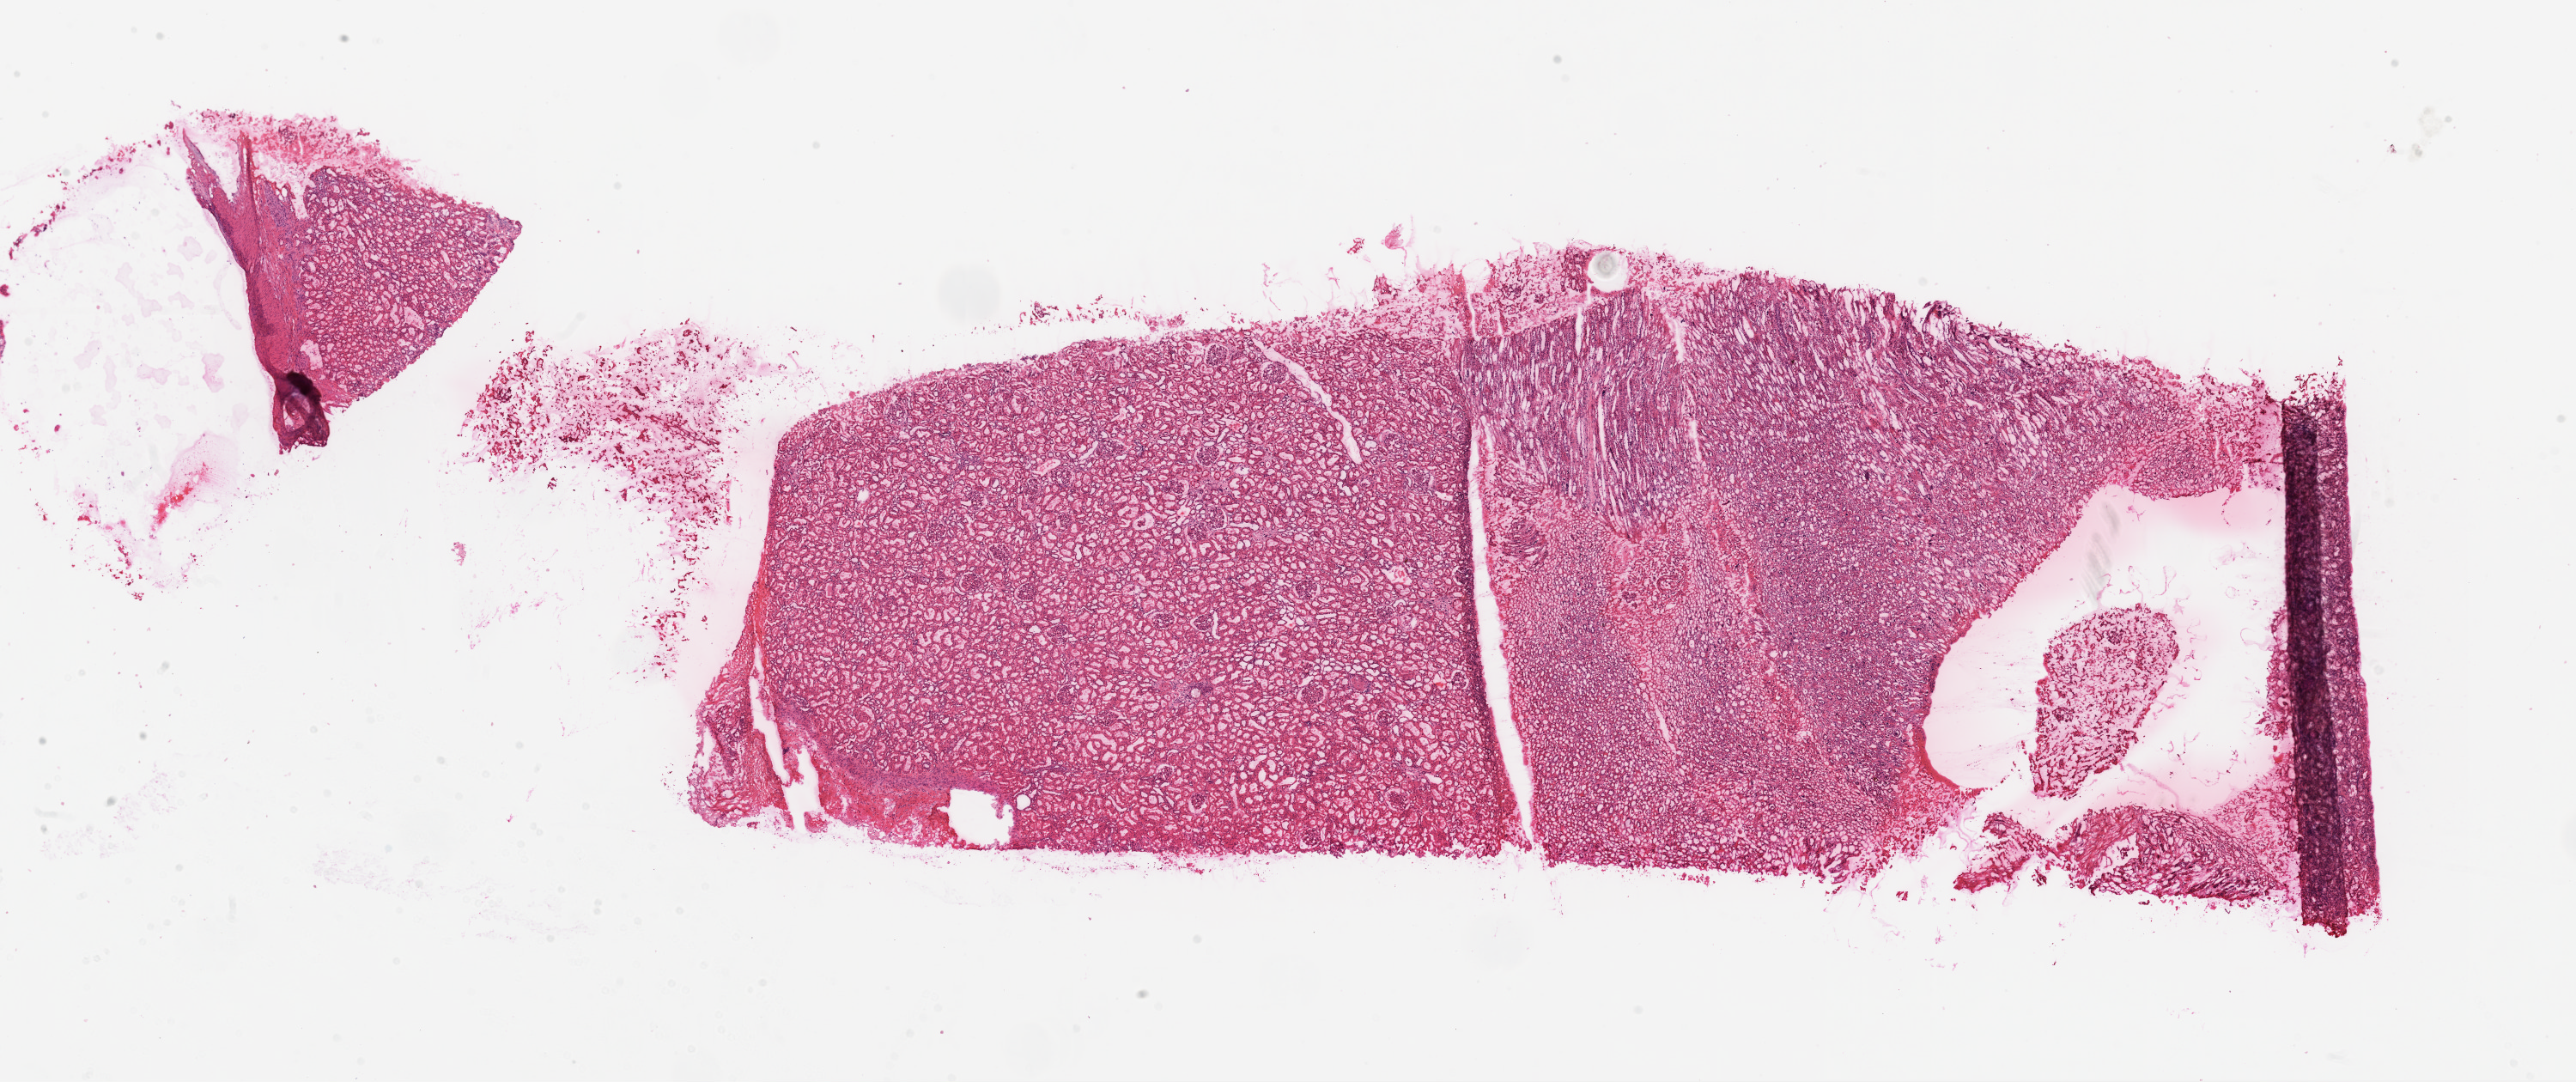
H&E whole-slide image — a low-resolution overview of the entire scanned area, about 24.1 x 10.1 mm (slide scanned at 20x). Frozen section from the top of the tissue portion. Solid tissue normal (non-tumour tissue) sample from the kidney. Male patient; age at initial diagnosis 51 years.
* this section: solid tissue normal (non-tumour) sample from the same patient
* patient diagnosis: Clear cell adenocarcinoma, NOS